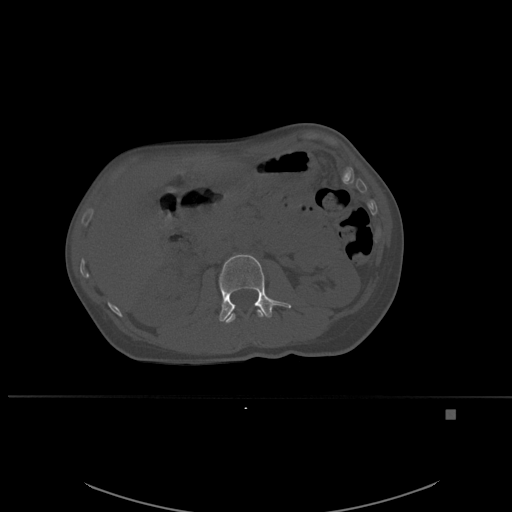
CT including the spine, one axial slice. Slice 242 of 537 in the series (ordered by position). Bone window (W 1800 / L 400 HU). 1.5 mm slice thickness. 512 × 512 image matrix, field of view 440 × 440 mm. Female patient, age 45 years. Case-level facts recorded for this patient, not image findings: primary cancer: lung.
Annotated regions visible in this slice (semi-automatic segmentation, software-assisted and operator-edited):
- L1 vertebra: bounding box [x1, y1, x2, y2] px = [224, 309, 264, 324]
- L2 vertebra: [219, 254, 292, 322]